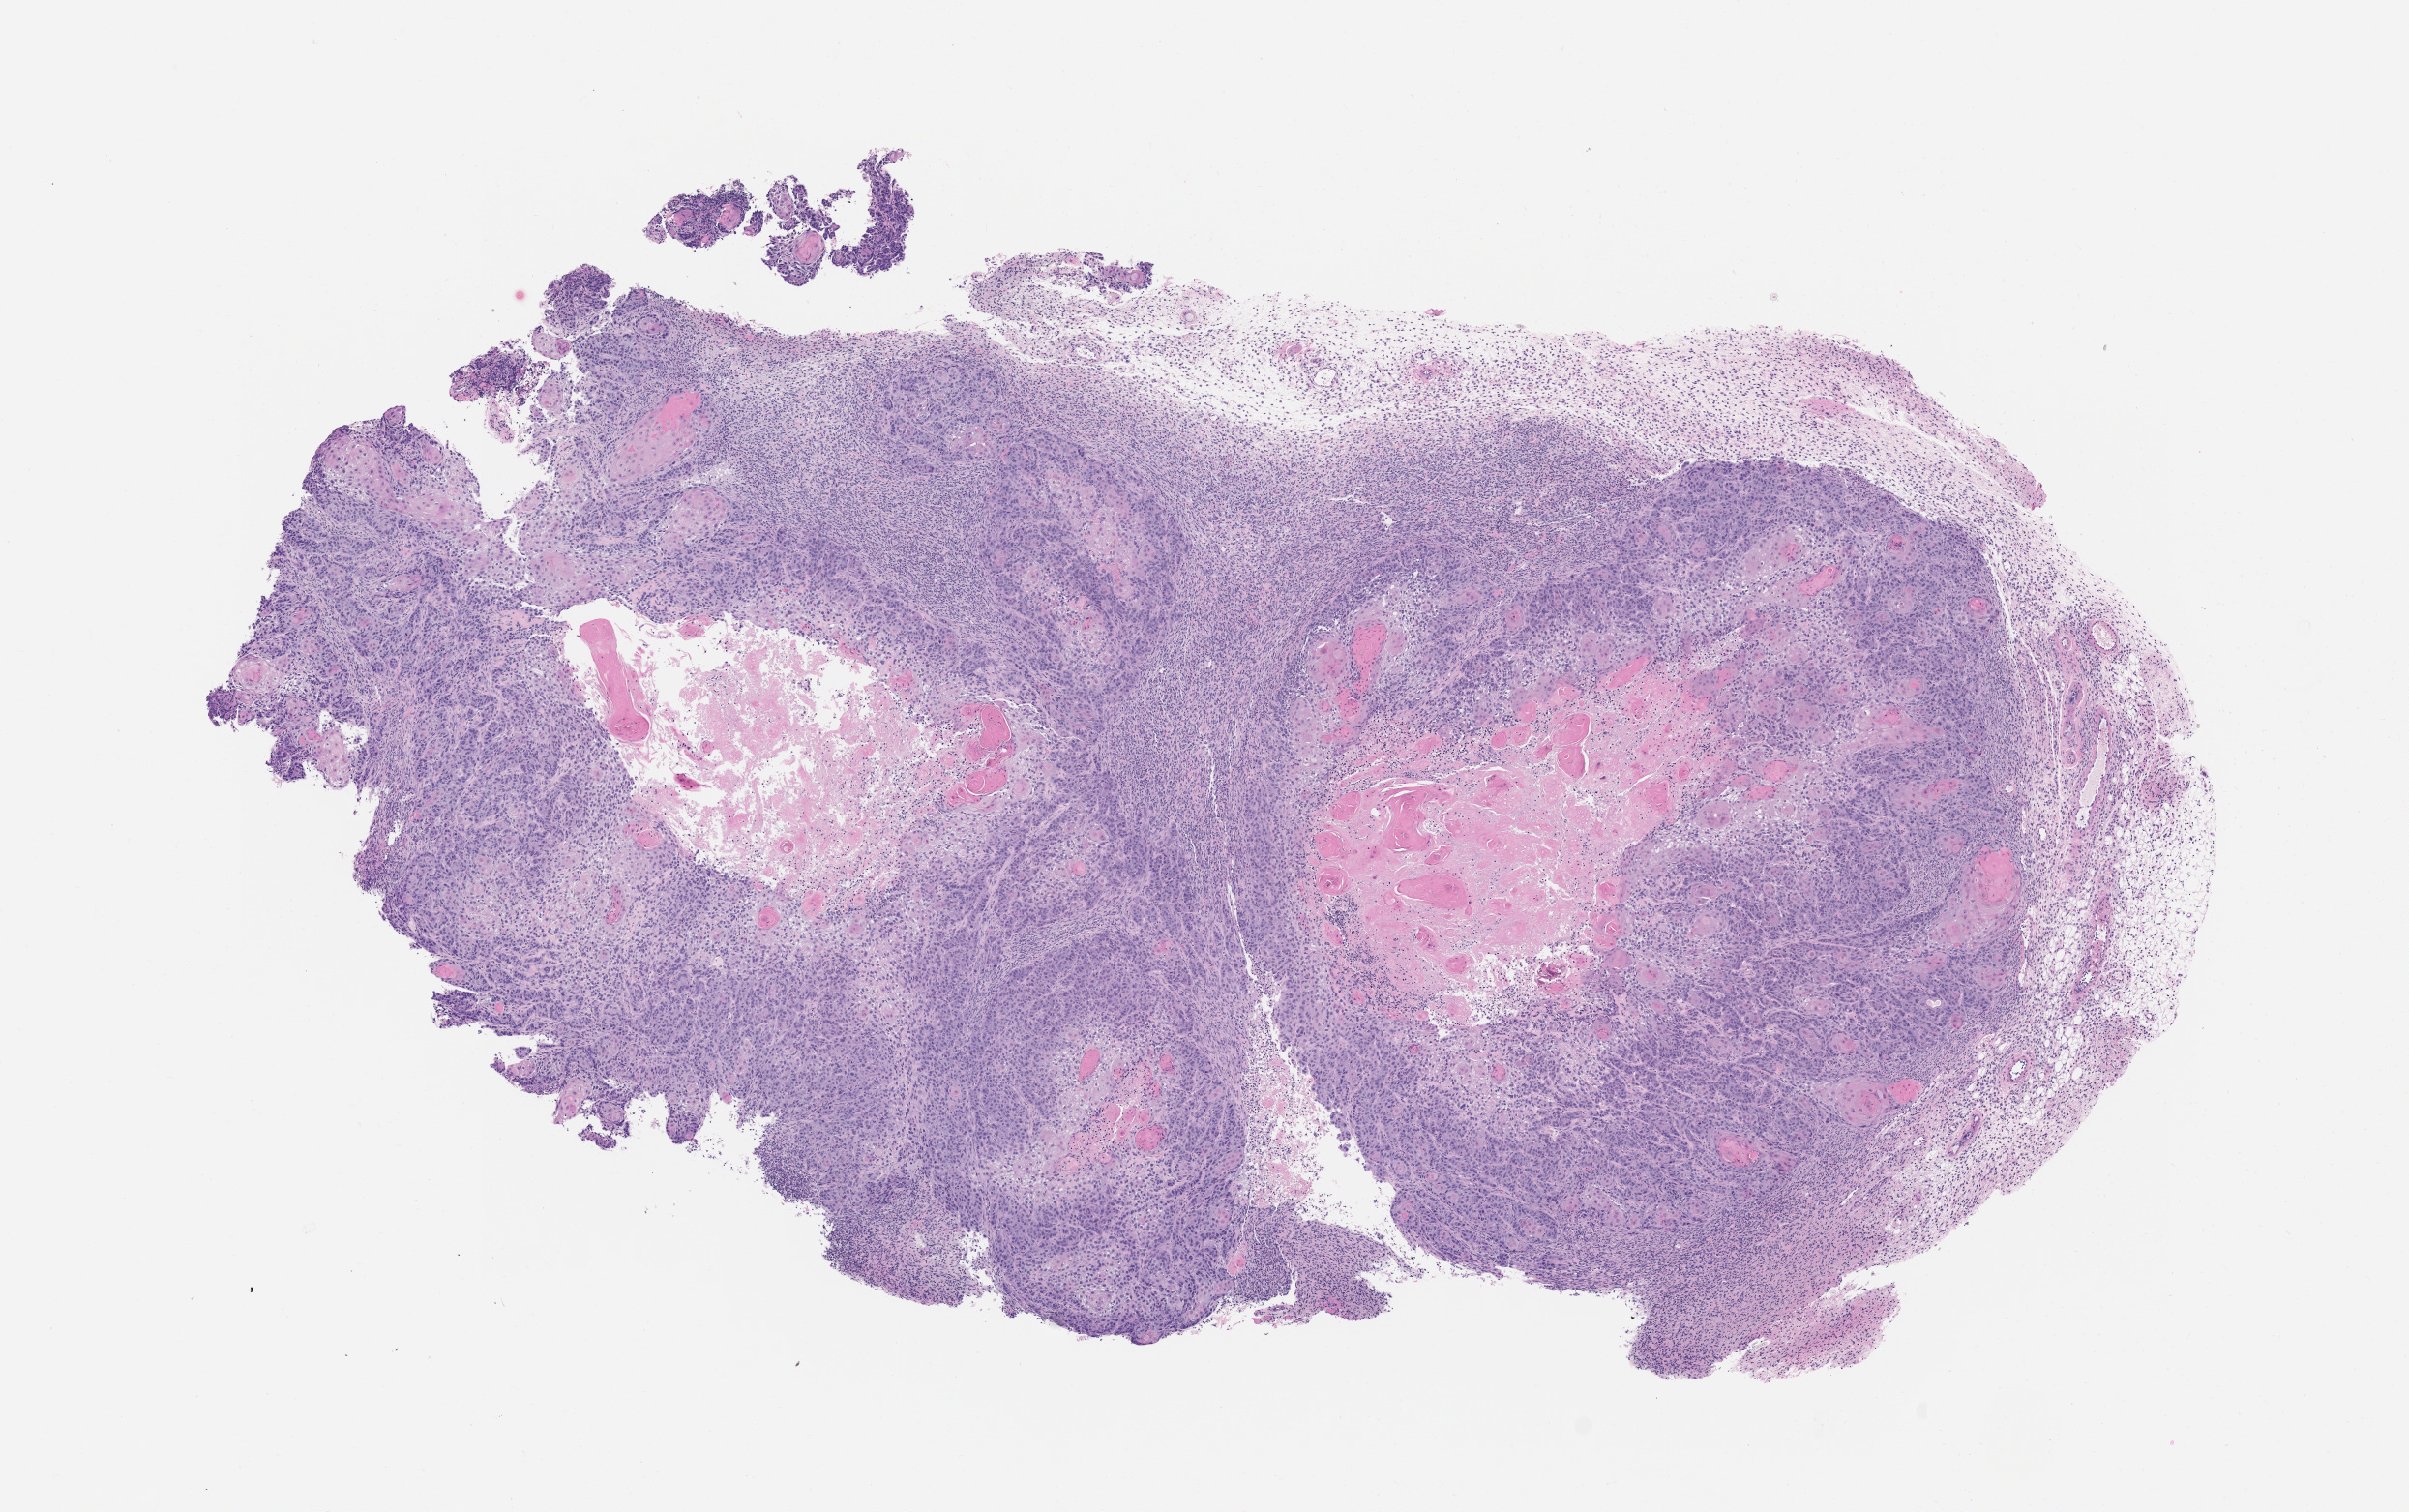
Whole-slide image, haematoxylin and eosin: patient-derived xenograft (human tumor grown in a mouse), passage 2, a low-resolution overview of the entire scanned area, about 10.0 x 6.3 mm; formalin-fixed paraffin-embedded section; tumor site category: oral soft tissue.
- originating patient diagnosis: Head and Neck Squamous Cell Carcinoma